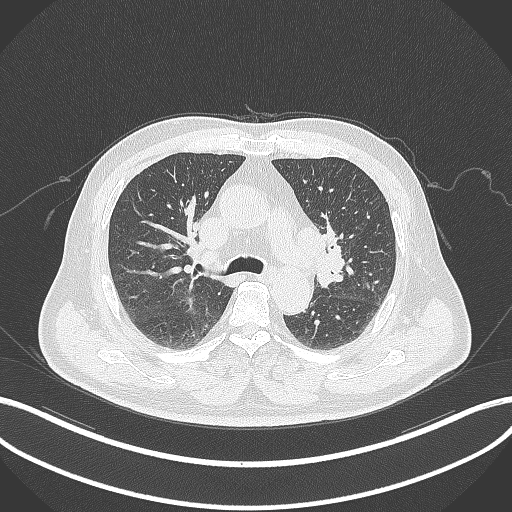
Chest CT, one axial slice; slice 192 of 286 in the series (ordered by position); reconstruction kernel B70f; lung window (W 1500 / L -600 HU); 1 mm slice thickness; 512 × 512 image matrix, field of view 400 × 400 mm. Male patient, age 67 years. From the clinical record (not read from this slice): clinical TNM (as recorded): T2a N1 M0; histopathological grade: G3.
Annotated regions visible in this slice (rectangle marked by the reading radiologist):
- lung tumour (recorded histology: adenocarcinoma): box from (x=323, y=218) to (x=344, y=273) px